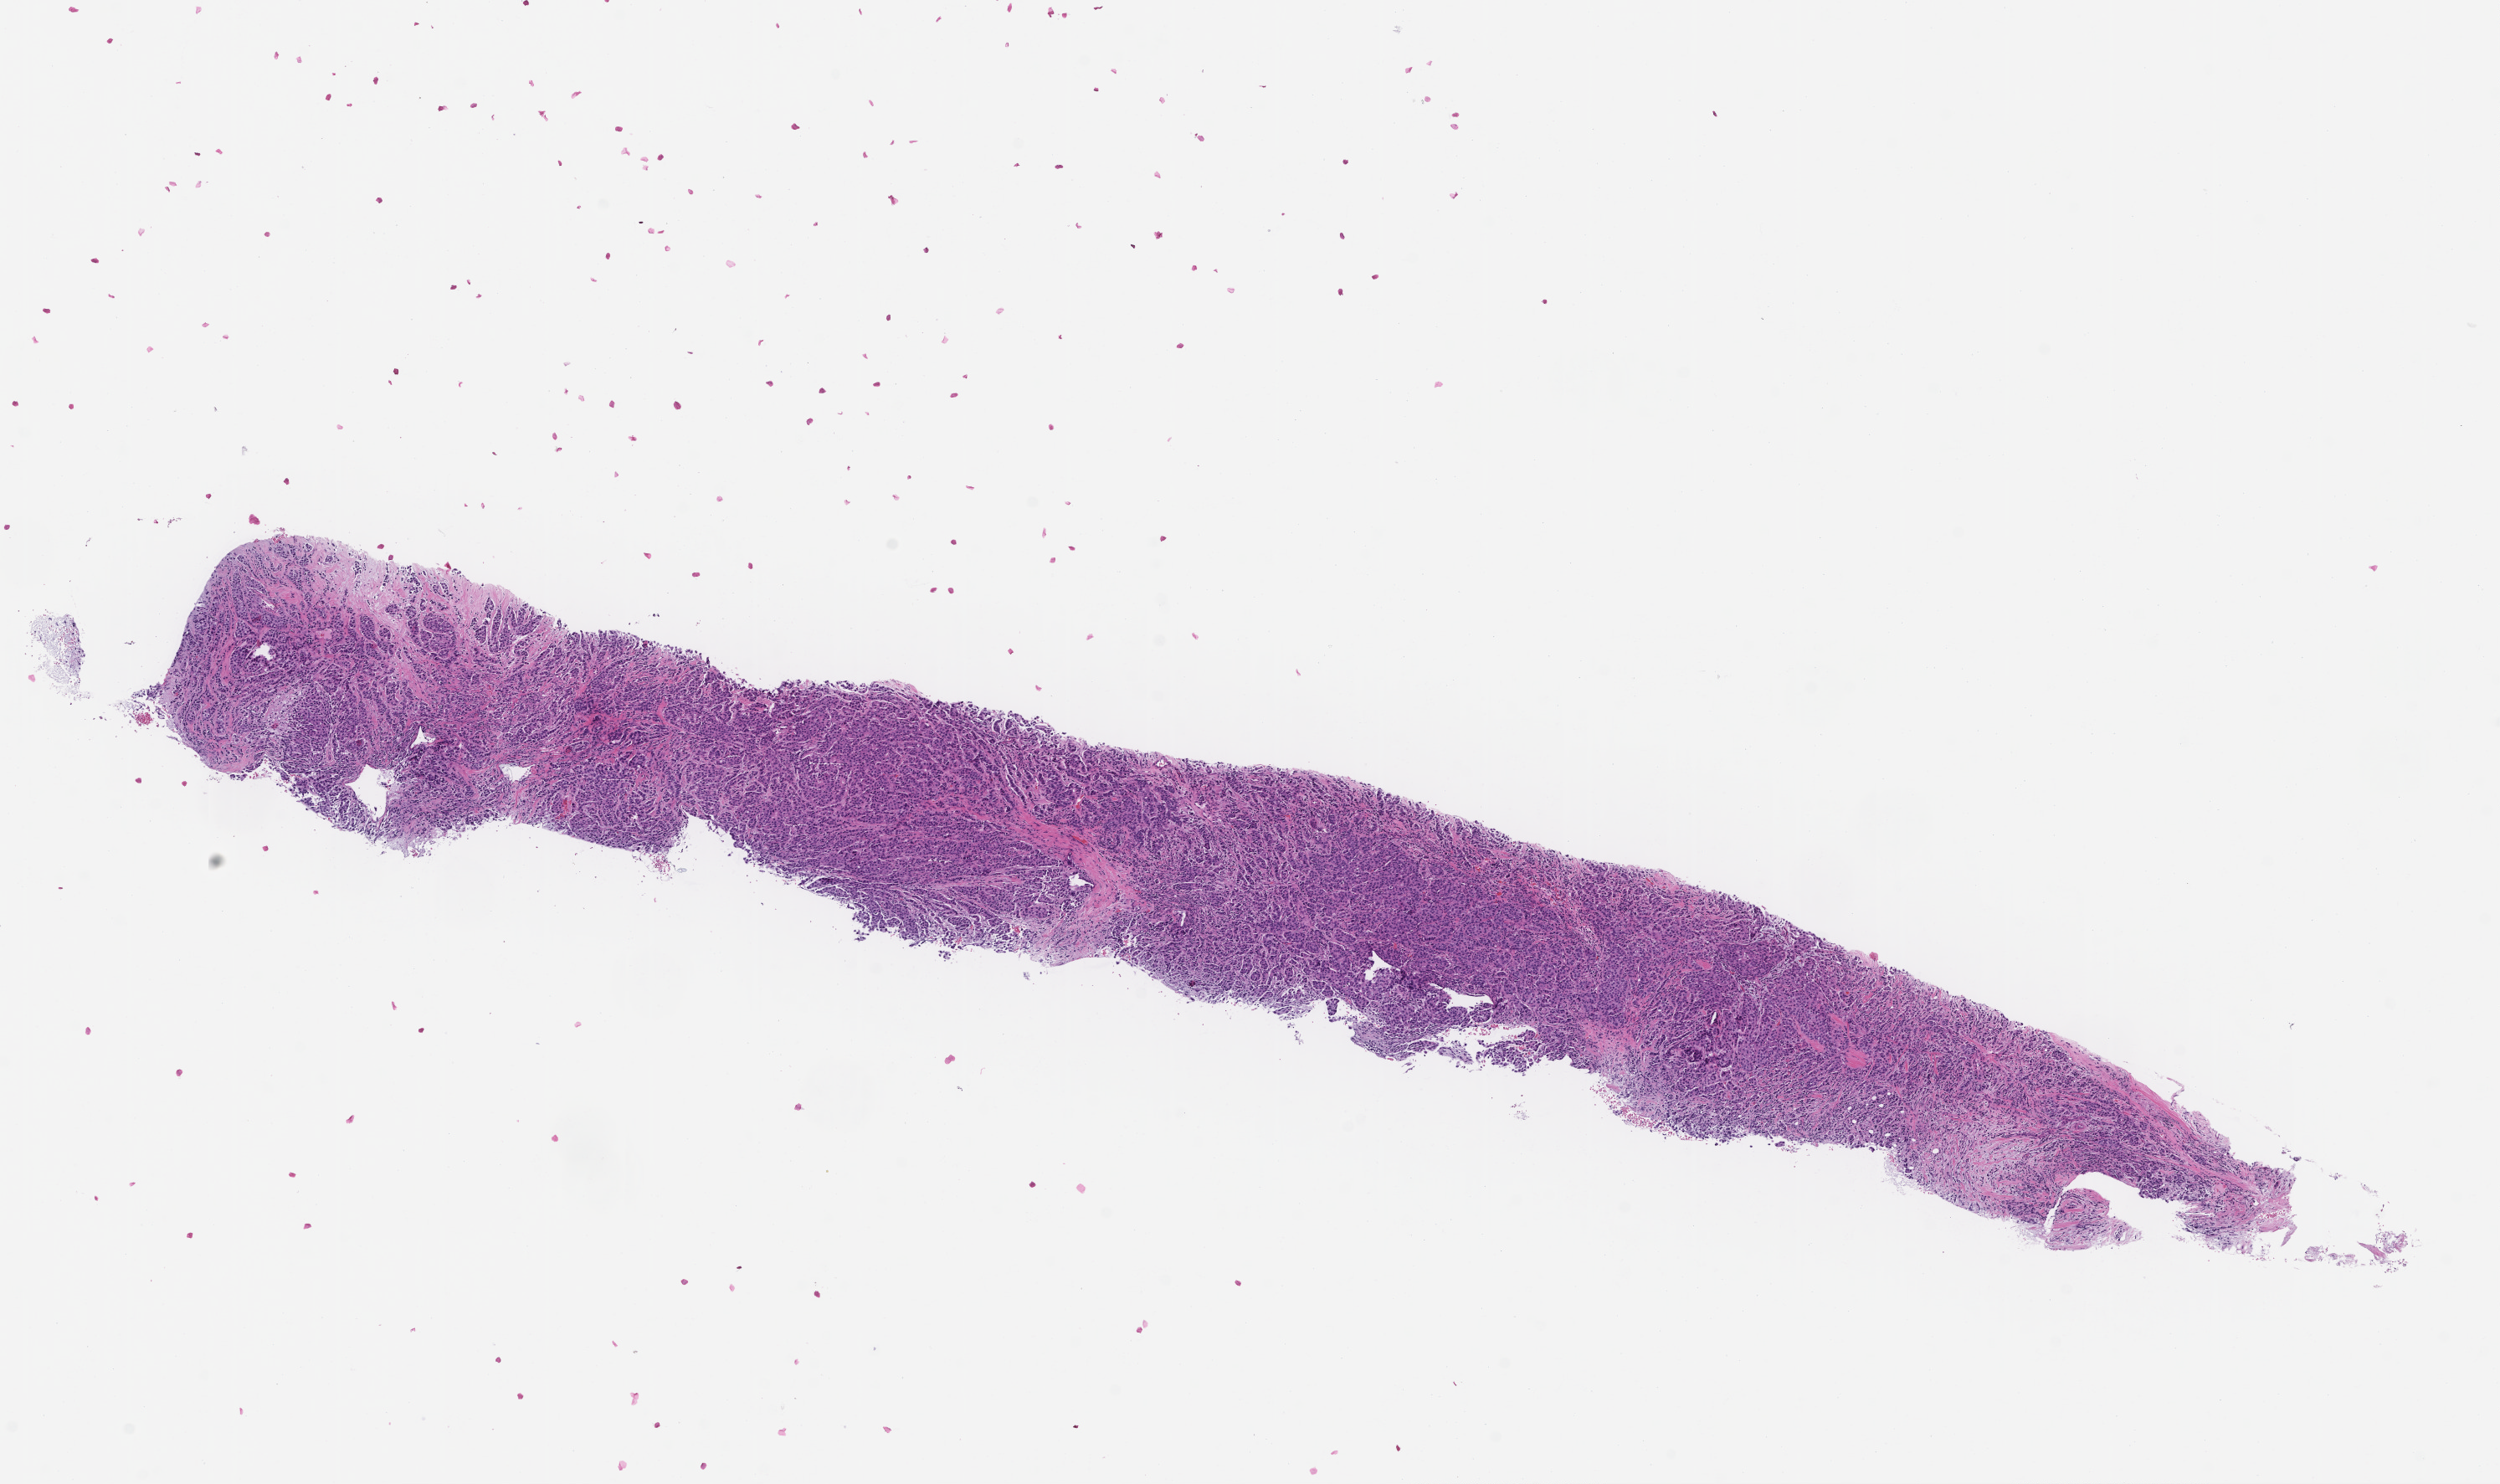
Hematoxylin and eosin (H&E) whole-slide image, a low-resolution overview of the entire scanned area, about 12.1 x 7.2 mm. Formalin-fixed, paraffin-embedded (FFPE) tissue. Tissue site: breast. Specimen time point: collected at baseline (before treatment). Female patient.
- this section: primary tumour tissue
- diagnosis: Invasive Breast Carcinoma